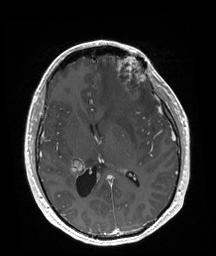
Brain MRI from a brain-tumour surgery series, one axial slice. Position 90 of 192 along the scan axis. T1-weighted post-contrast. 1 mm slice thickness. 216 × 256 image matrix. Case-level facts recorded for this patient, not image findings: tumour location: Left Frontal.
Annotated regions visible in this slice (expert manual segmentation):
- tumour: bounding box <116,56,146,99> (left, top, right, bottom; pixels)